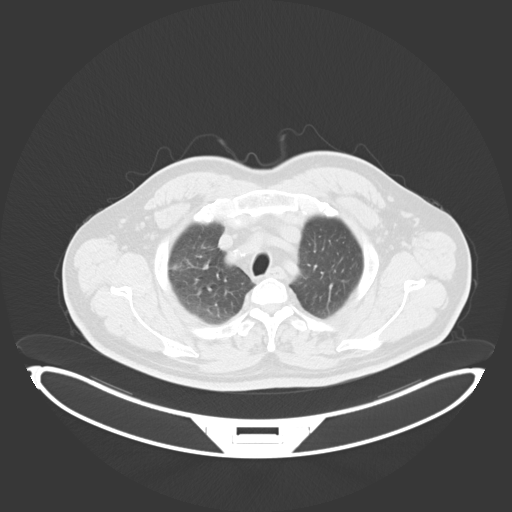
Chest CT, one axial slice. Position 231 of 284 along the scan axis. 120 kVp. Lung window (W 1500 / L -600 HU). 3 mm slice thickness. 512 × 512 image matrix. Male patient, age 55 years. From the clinical record (not read from this slice): clinical TNM (as recorded): T3 N2 M1.
Structures marked on this image (bounding box drawn by a radiologist):
- lung tumour (recorded histology: adenocarcinoma): bounding box [x1, y1, x2, y2] px = [169, 258, 189, 278]